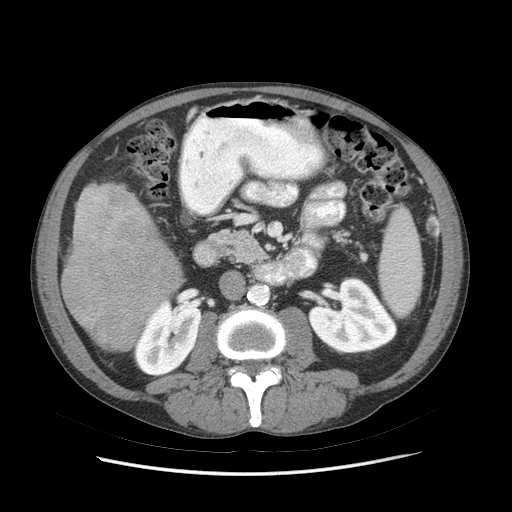
Contrast-enhanced abdominal CT (liver protocol), one axial slice; position 23 of 89 along the scan axis; reconstruction kernel STANDARD; soft-tissue window (W 400 / L 40 HU); 512 × 512 image matrix, field of view 380 × 380 mm. Case-level facts recorded for this patient, not image findings: diagnosis: hepatocellular carcinoma (patient treated with transarterial chemoembolisation; whether this scan precedes or follows treatment is not stated here); TNM stage (as recorded): Stage-IIIB; Child-Pugh class: A; tumour differentiation: moderately differentiated.
Annotated regions visible in this slice (semi-automatically segmented with operator editing):
- liver parenchyma outside the tumour (the mass and vessels are separate outlines, so this box may not span the whole liver): box from (x=62, y=182) to (x=182, y=326) px
- mass: (x=62, y=219)–(x=178, y=353)